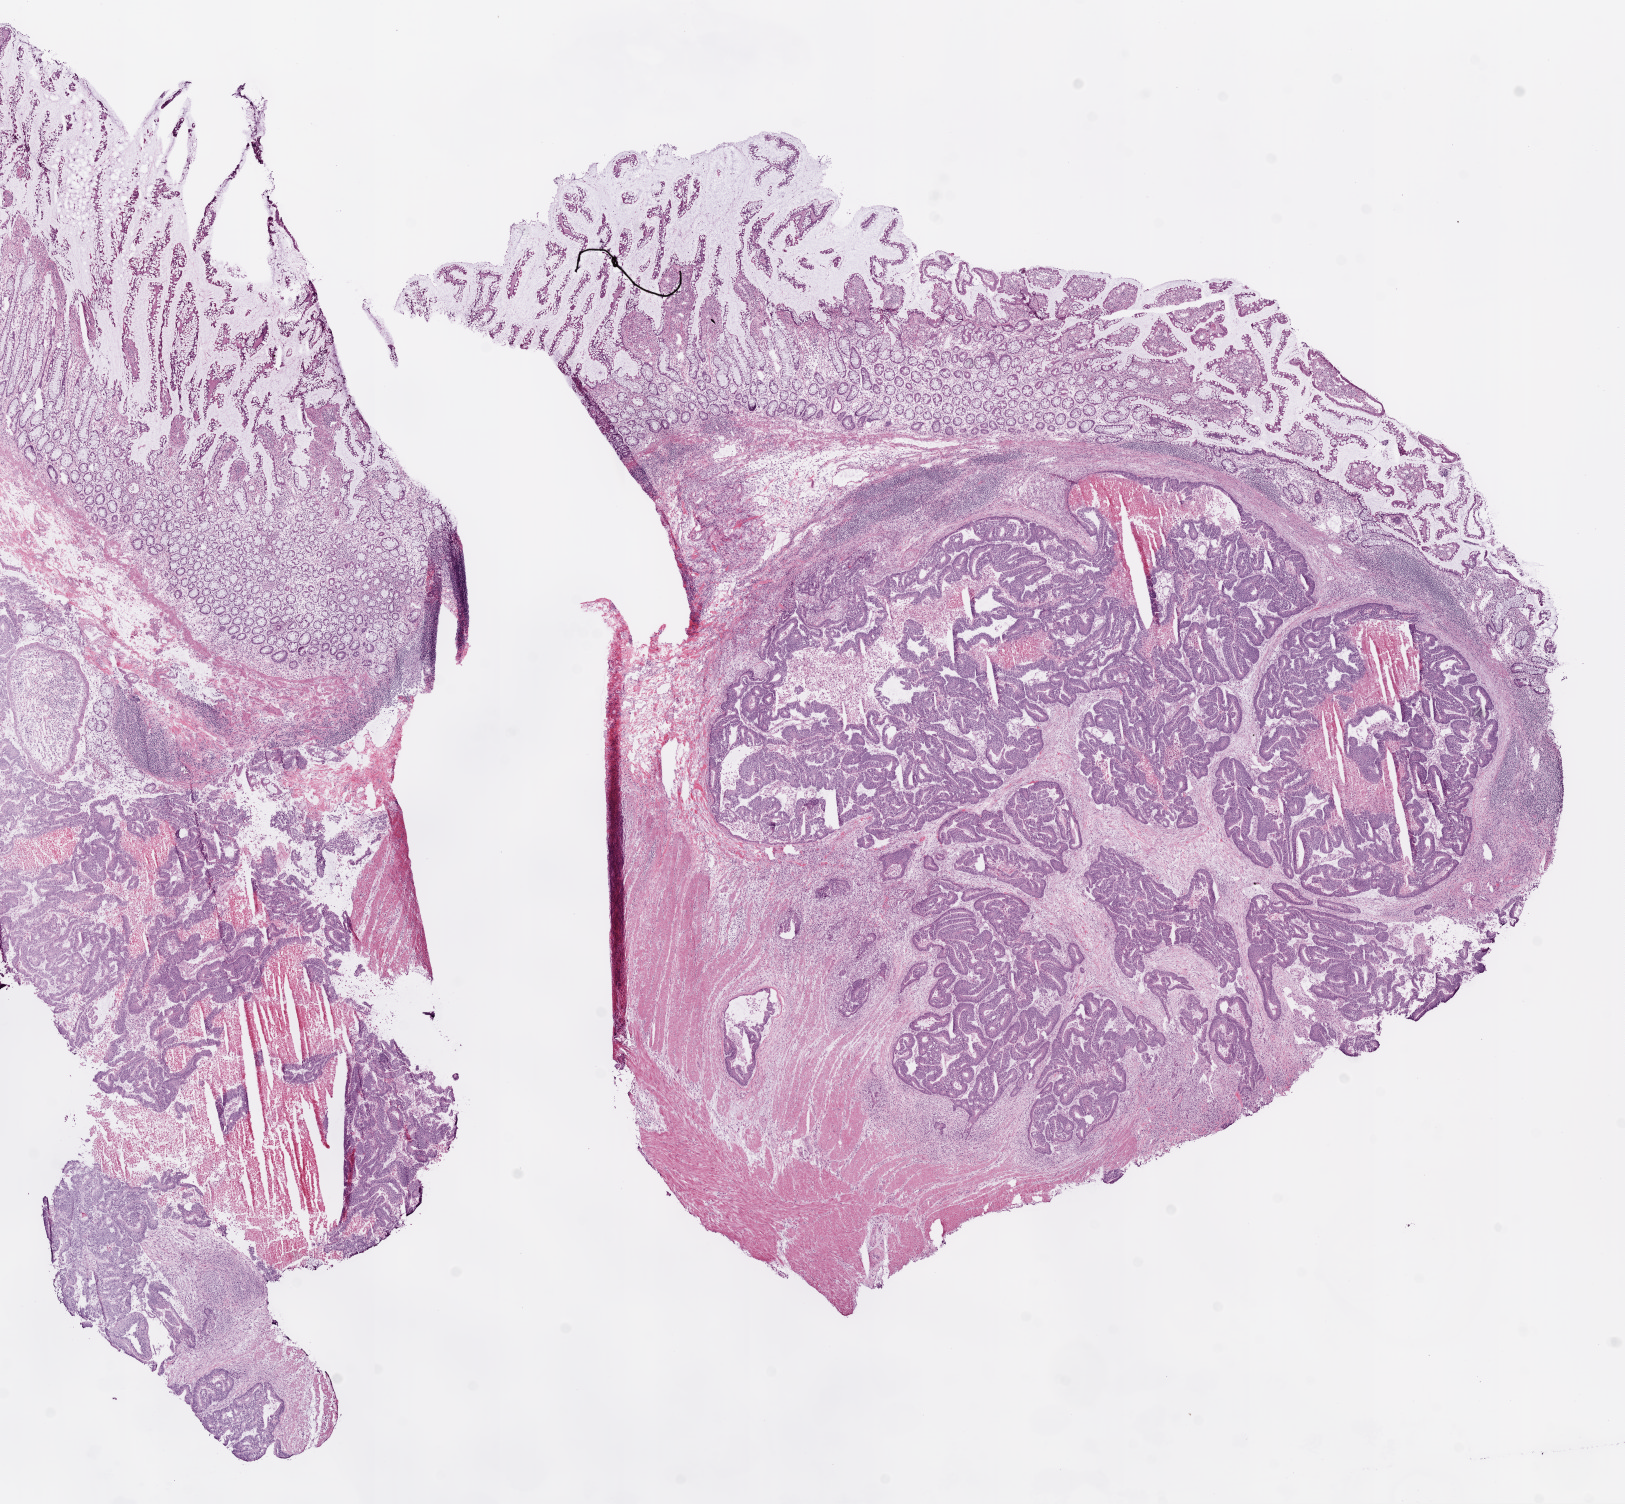
Digitized H&E tissue section (whole slide), low-resolution overview of the scanned area, about 13.0 x 12.1 mm; frozen section; primary tumour sample from the colon. Female, age 68 years at initial diagnosis. Composition of this section per pathologist review: tumour cells 57%, tumour nuclei 60%, normal cells 33%, stromal cells 0%, necrosis 10%. Infiltration values recorded for this section: lymphocyte infiltration 10%, monocyte infiltration 1%, neutrophil infiltration 2%.
AJCC pathologic stage: IIA (7th edition). Histologic diagnosis: Adenocarcinoma, NOS (cecum). TNM: T3 N0 M0. Lymph nodes positive (case pathology): 0 of 21 examined.